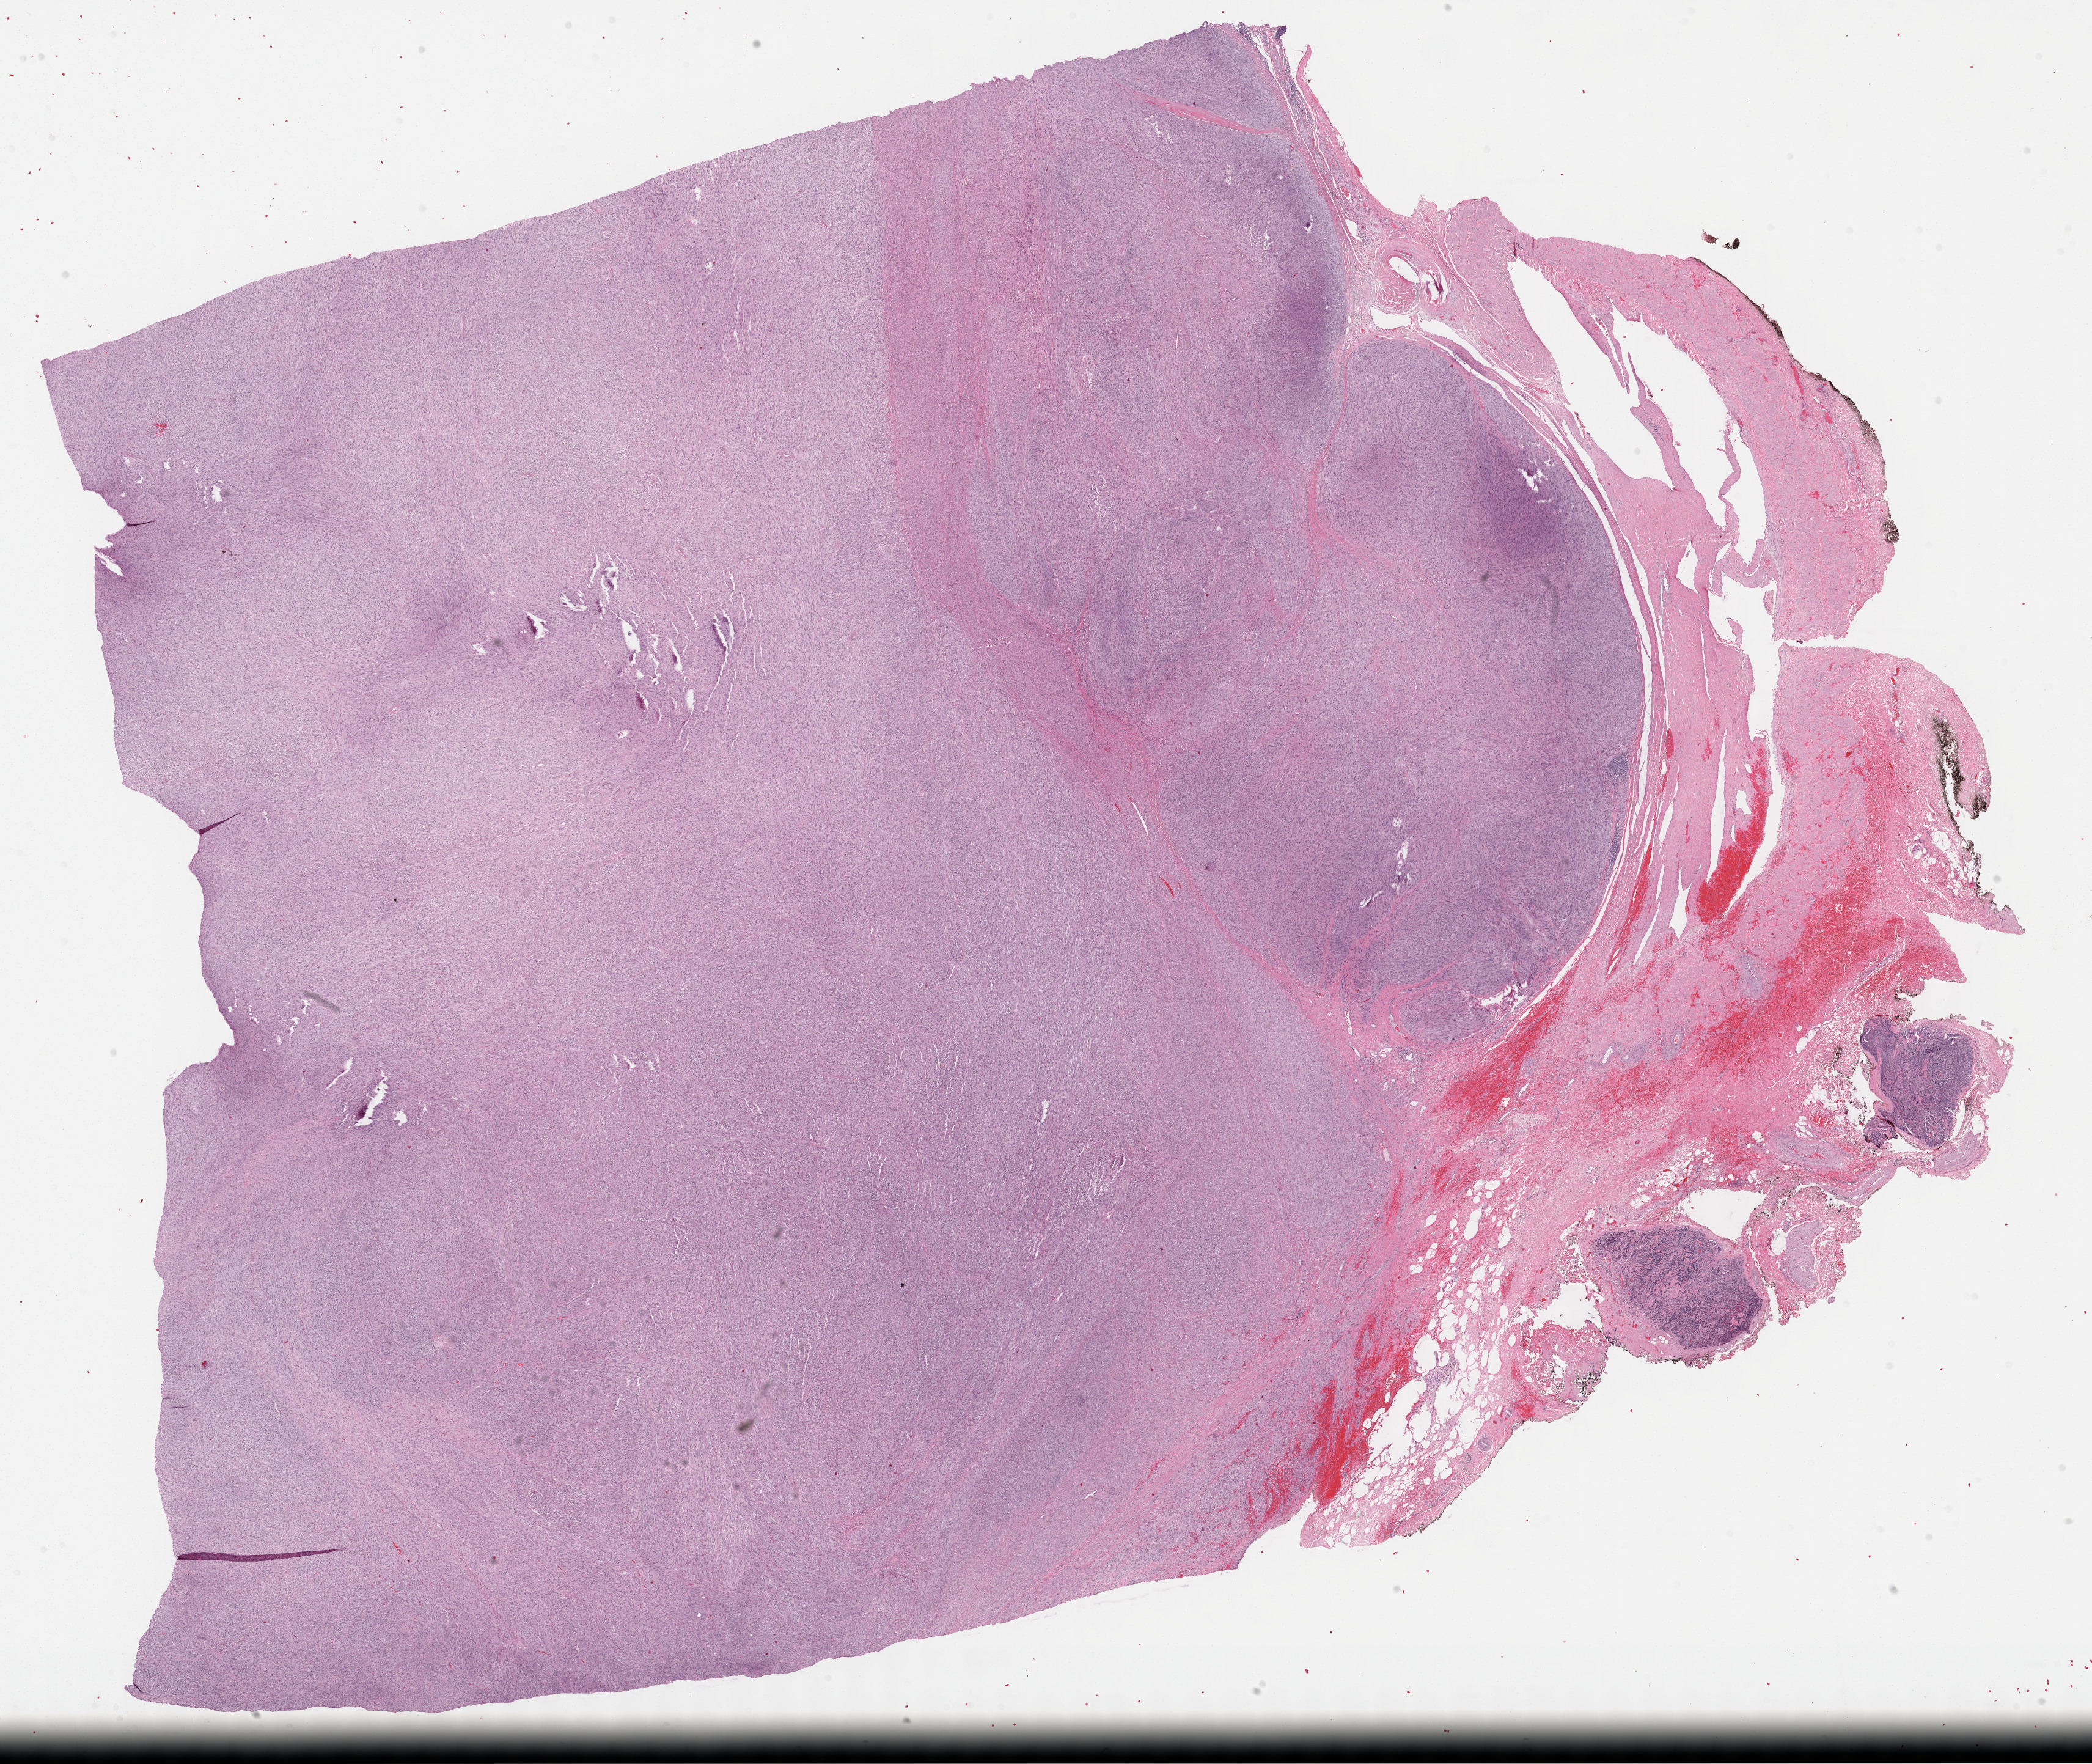
Whole-slide histology image, H&E, low-resolution overview of the scanned area, about 27.7 x 23.3 mm (slide scanned at 40x). Formalin-fixed paraffin-embedded (FFPE) diagnostic section. Primary tumour sample from the retroperitoneum and peritoneum. Patient: female, age at initial diagnosis 65 years.
Pathologic diagnosis: Leiomyosarcoma, NOS (retroperitoneum).